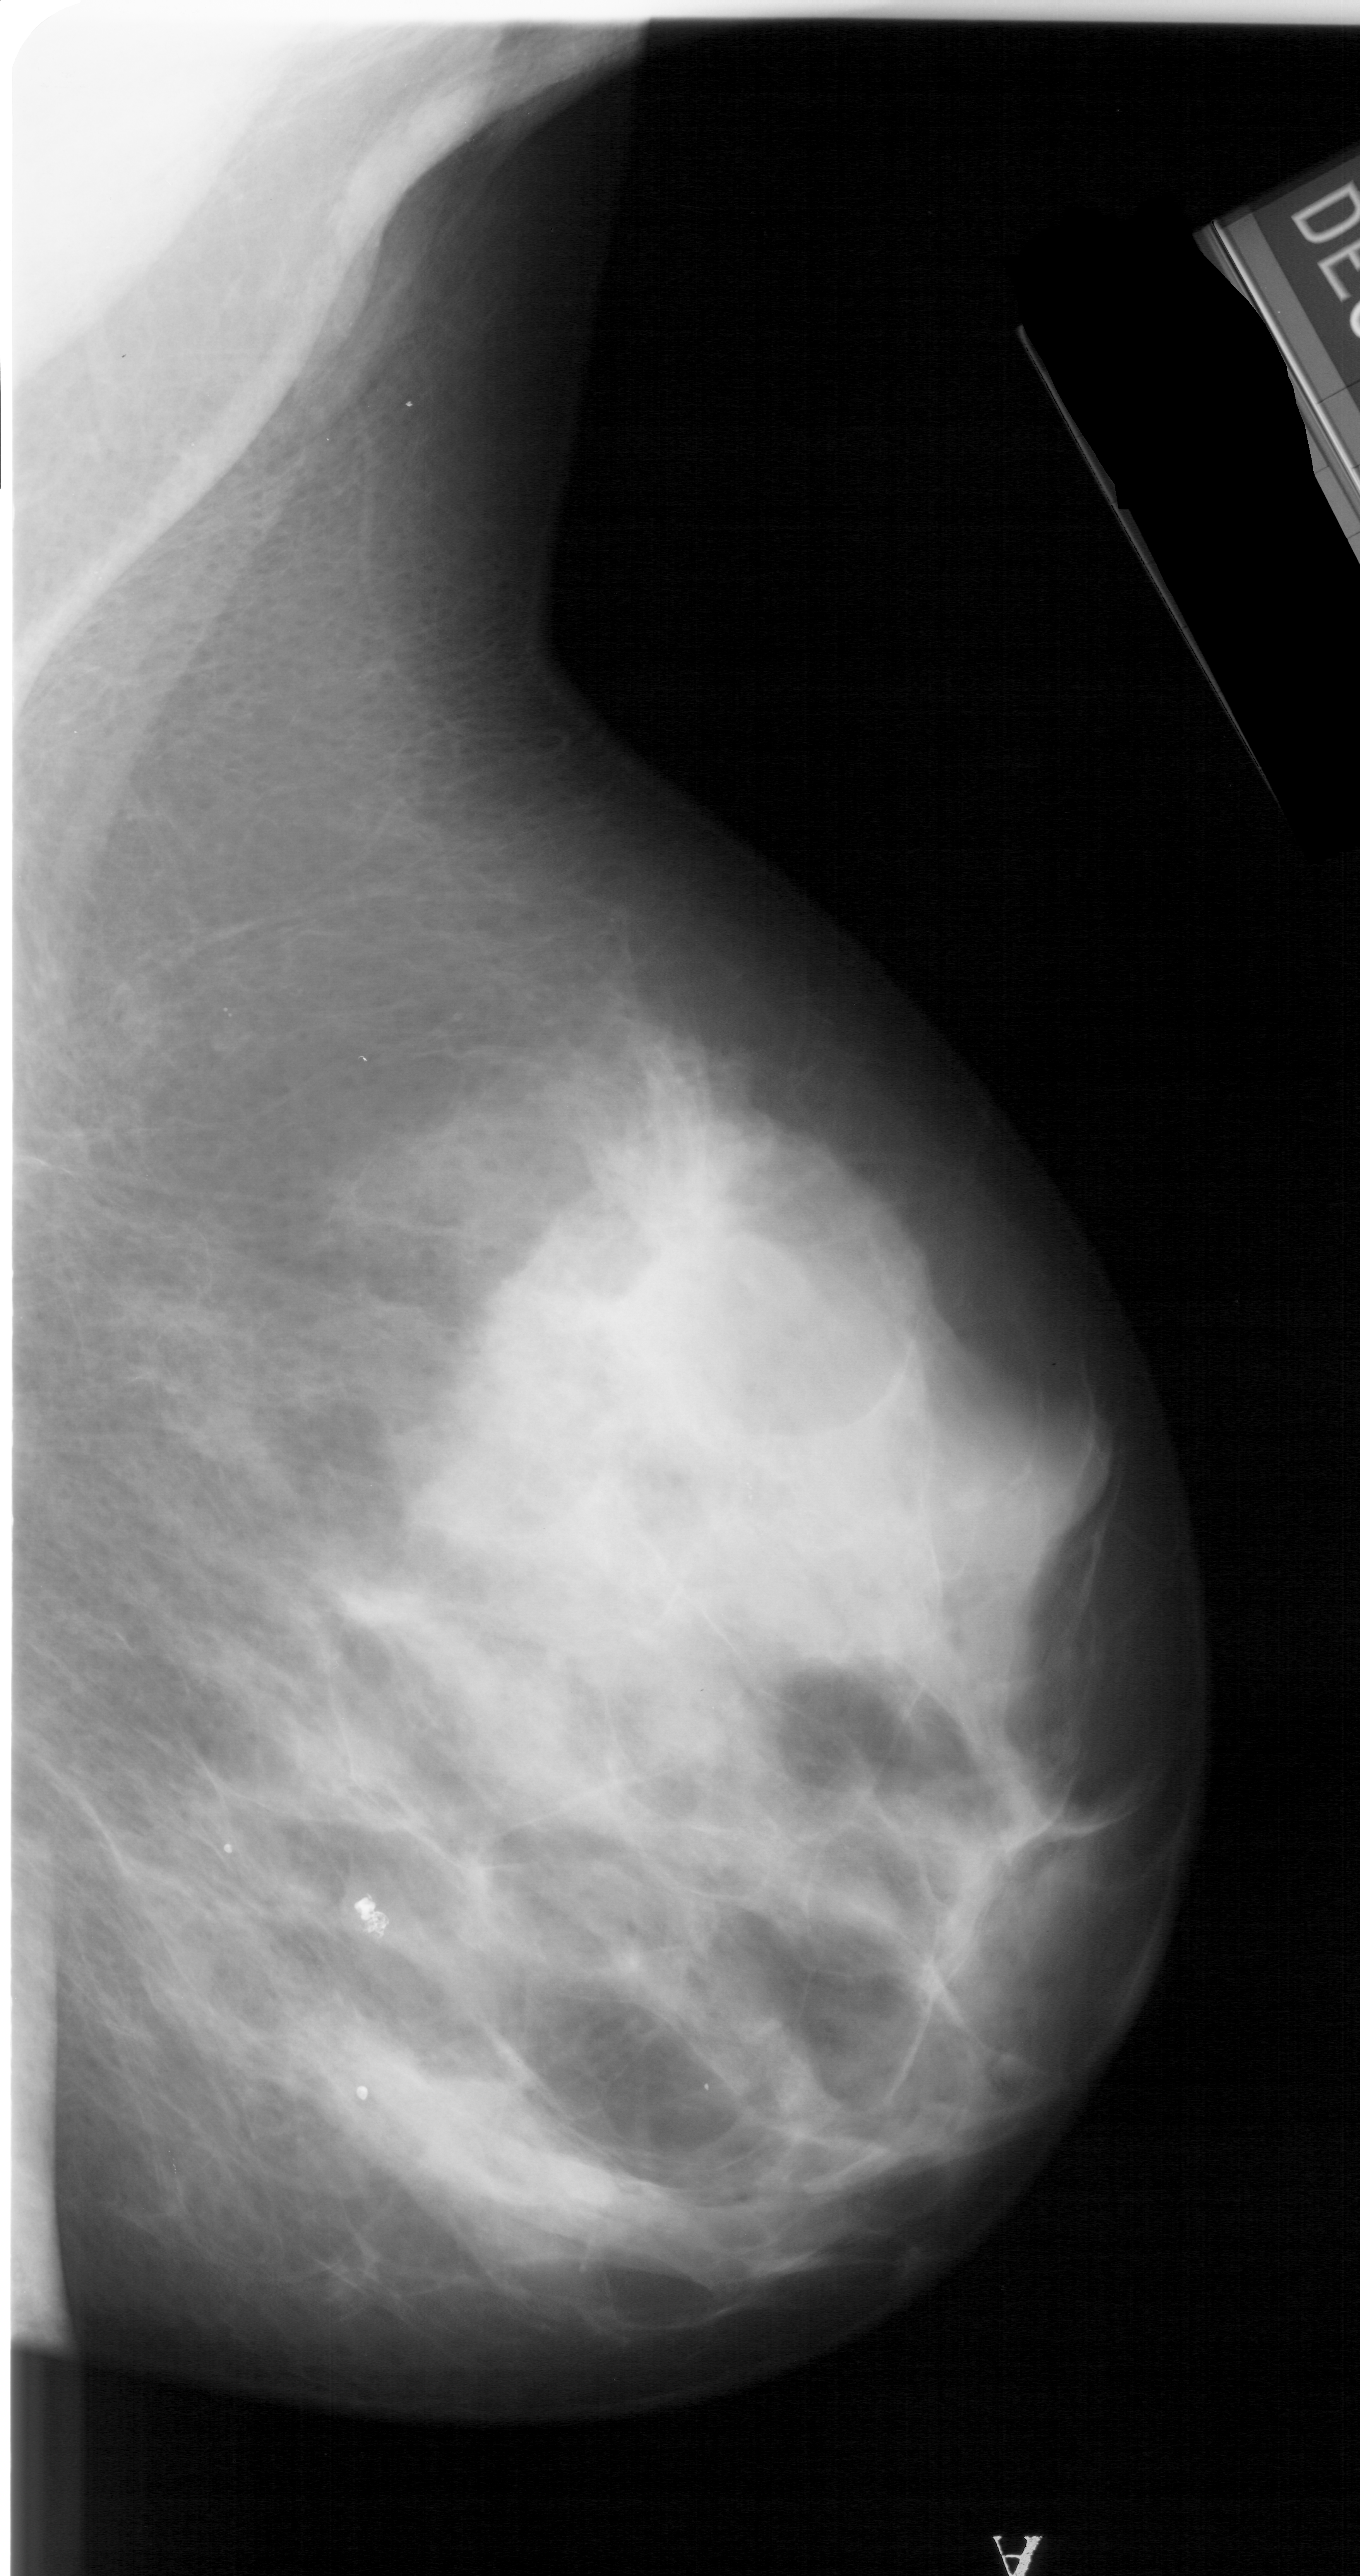
Mammogram (digitized film); right breast; mediolateral oblique (MLO) view; breast composition: extremely dense (BI-RADS density category 4 of 4); 1360 × 2576 image matrix.
Marked abnormalities (boxes around the expert regions of interest):
- calcifications, morphology punctate, distribution clustered; BI-RADS assessment category 3; subtlety rating 1 on a 1 (subtle) to 5 (obvious) scale; pathology result (as recorded, not read from the image): malignant: bounding box <723,1484,748,1525> (left, top, right, bottom; pixels)